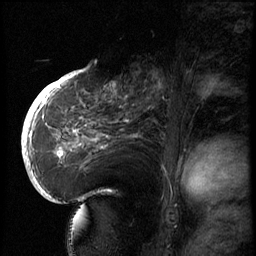
Breast MRI (dynamic contrast-enhanced), one sagittal slice; position 34 of 66 along the scan axis; 3 images stored at this slice position (order not interpretable as contrast timing); 1.5 T; TE 4.2 ms, TR 8.9 ms; 2.5 mm slice thickness; 256 × 256 image matrix, field of view 200 × 200 mm. Patient: female, 56 years. From the clinical record (not read from this slice): setting: breast cancer imaged before/during neoadjuvant chemotherapy.
Structures marked on this image (semi-automatically segmented with operator editing):
- analysis volume of interest (the breast-tissue region the enhancement analysis was run in; not a lesion): bounding box <129,62,194,127> (left, top, right, bottom; pixels)
- tumour enhancement mask (voxels above the 140 % enhancement threshold inside the analysis volume of interest): <129,72,167,123>